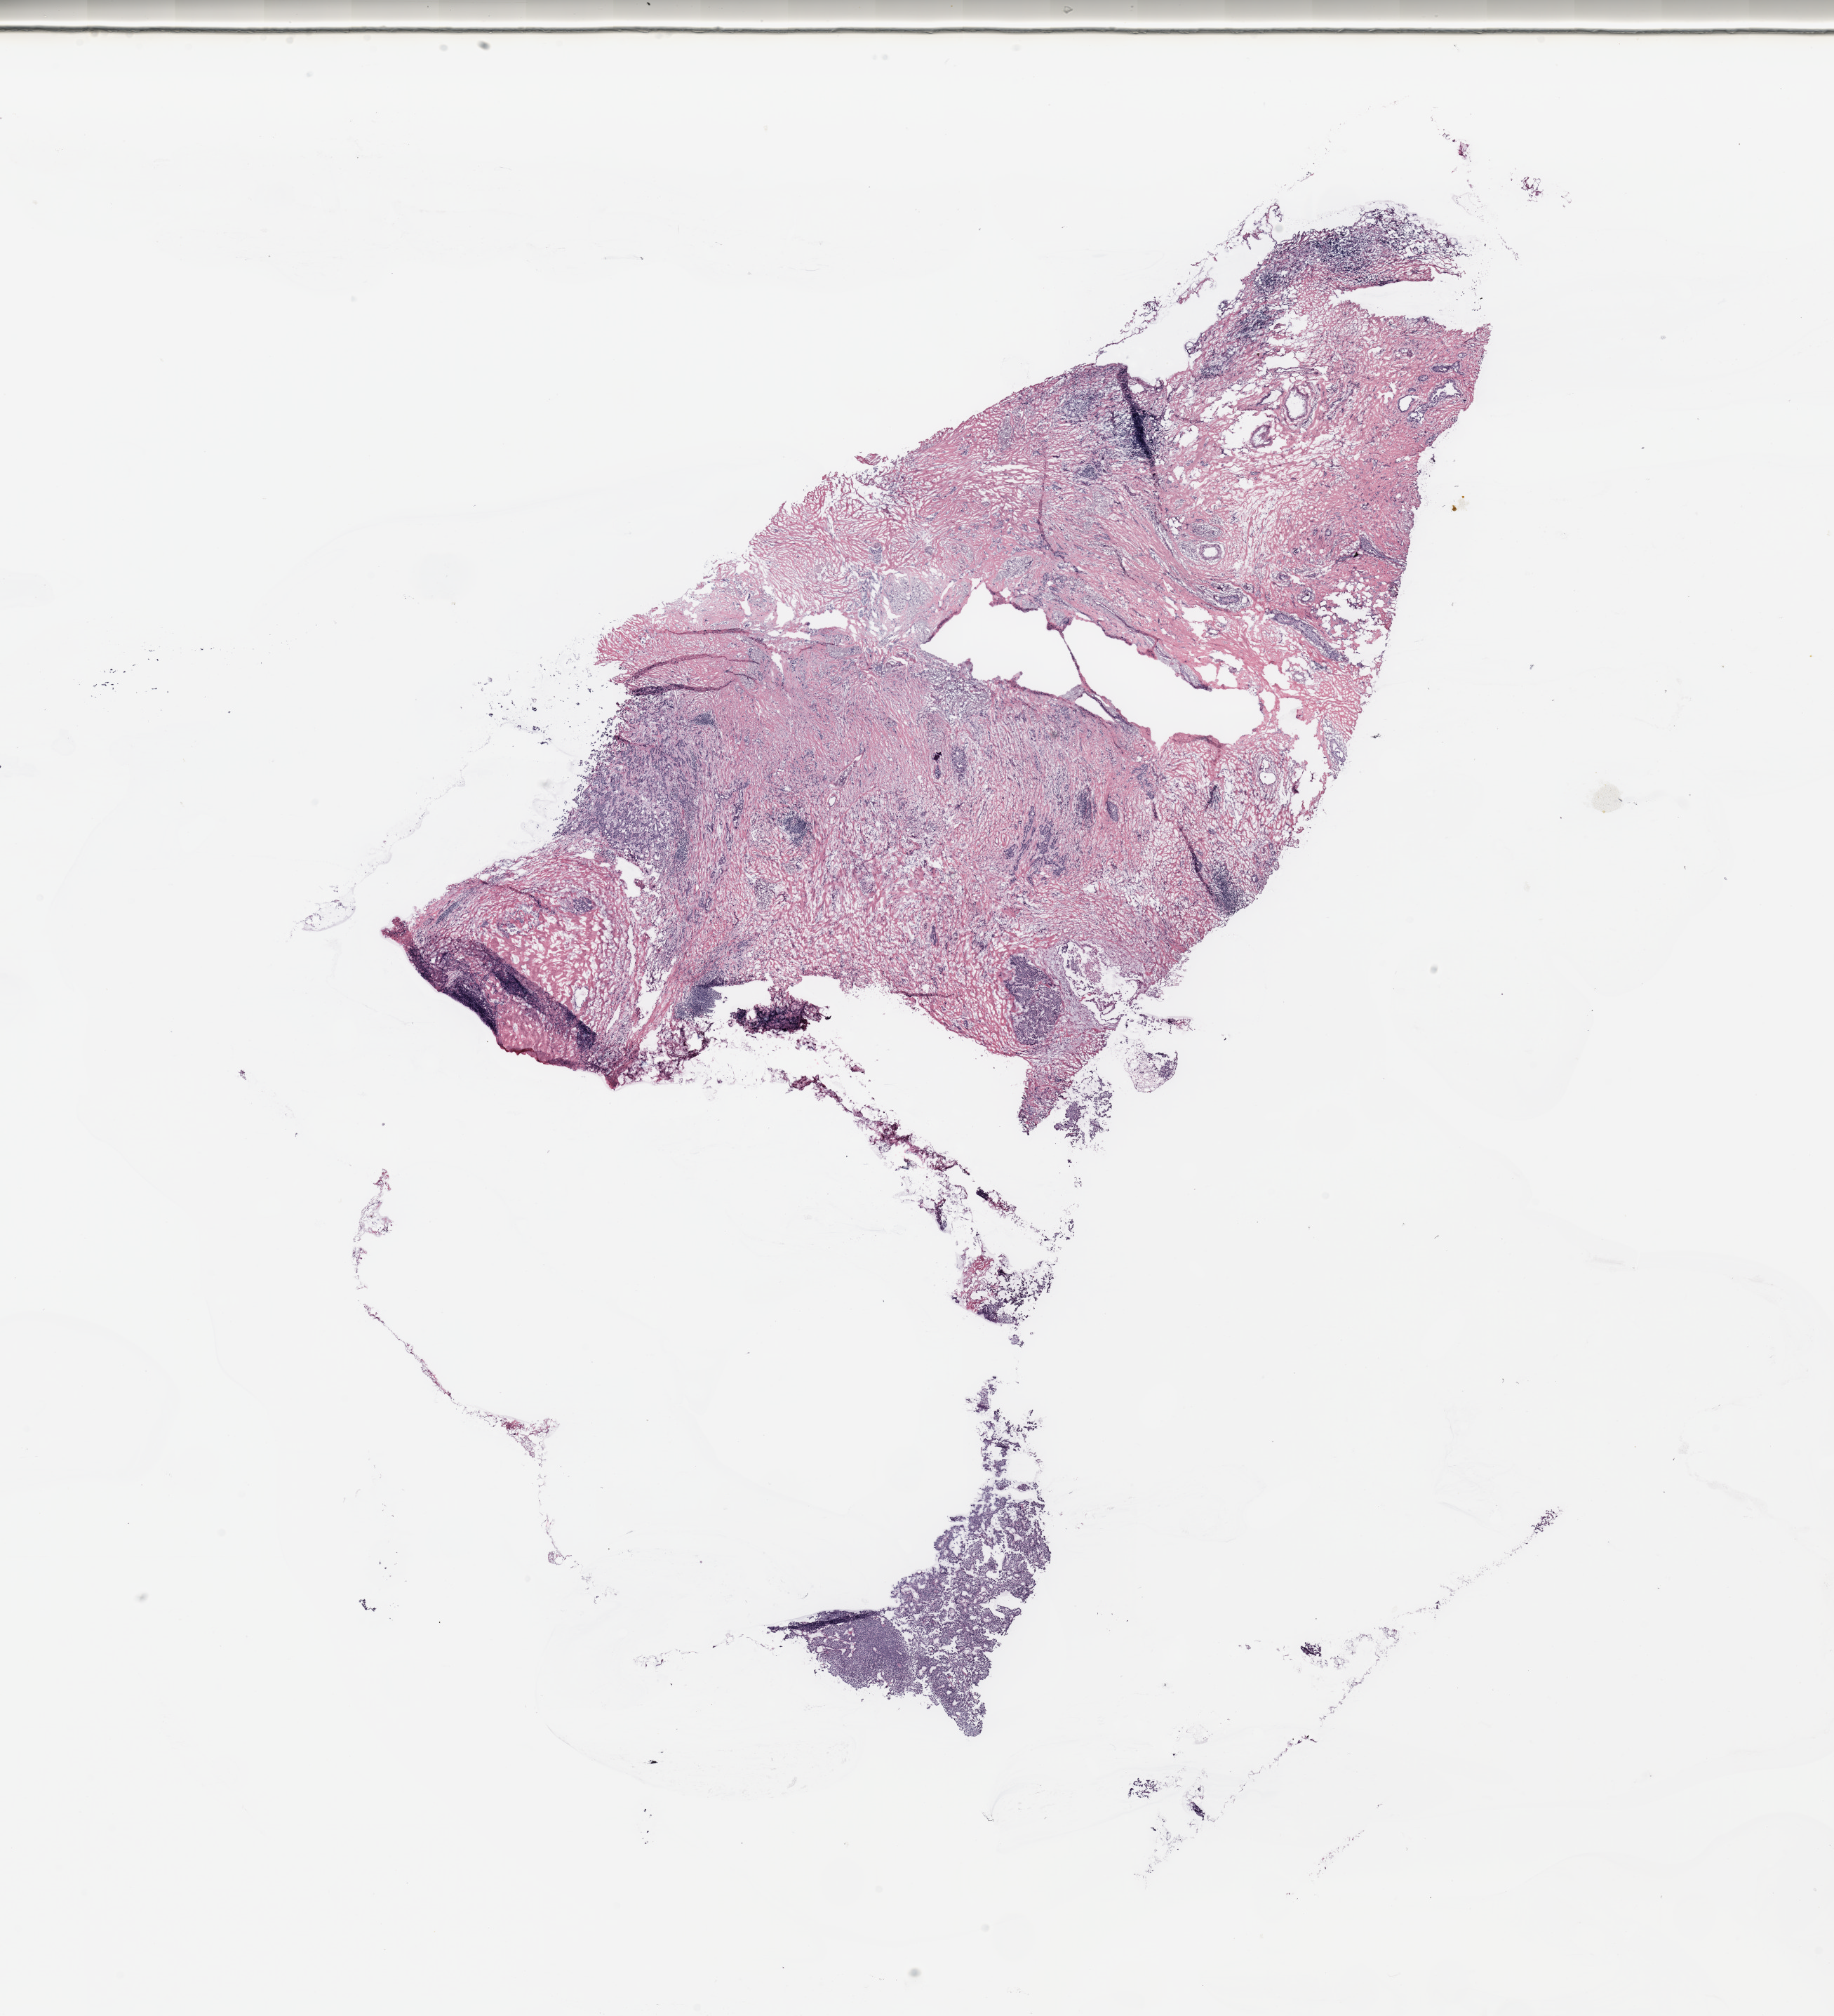
Digitized H&E-stained tissue section (whole slide), a low-resolution overview of the entire scanned area, about 20.7 x 22.7 mm (from a 20x scan); breast, tissue type not recorded.
Patient diagnosis (cohort enrolment): breast cancer (breast).